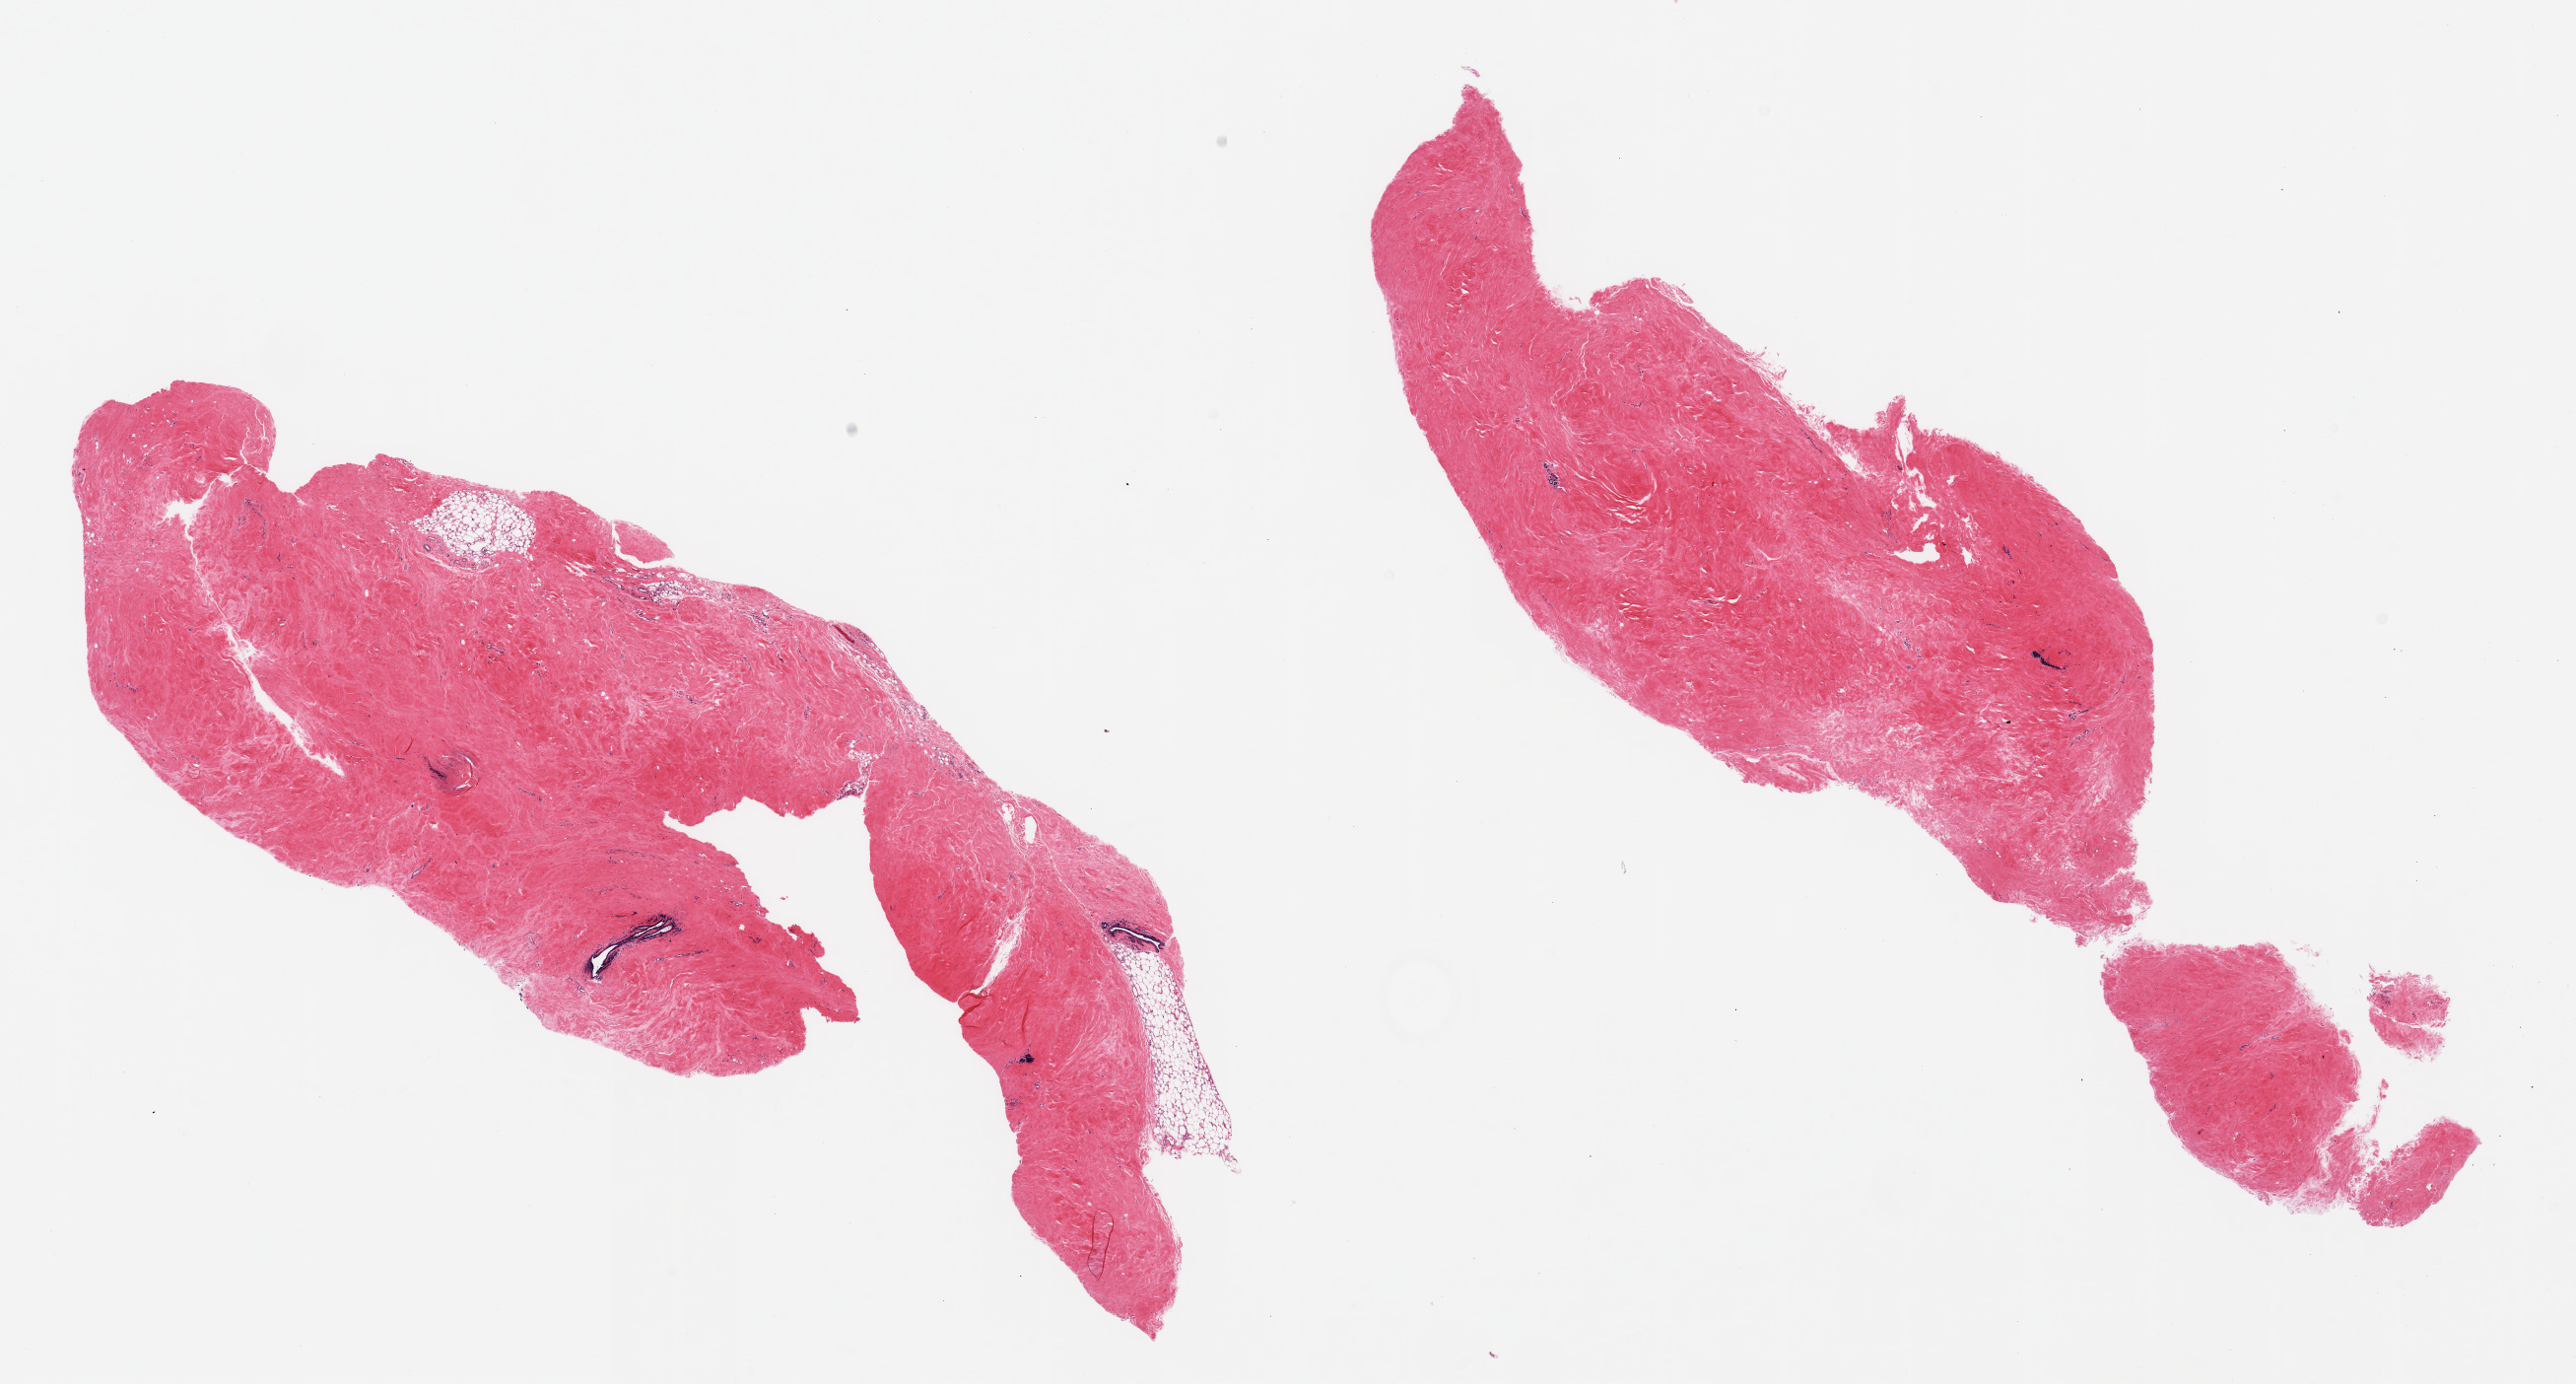
Digitized H&E-stained section — shown as a low-resolution overview of the whole scanned area (about 20.7 x 11.1 mm). PAXgene-fixed, paraffin-embedded tissue. Section of breast (target tissue). Donor tissue sample. Donor: male.
• pathologist's review note for this sample: 2 pieces; florid stromal and focal ductal gynecomastoid hyperplasia